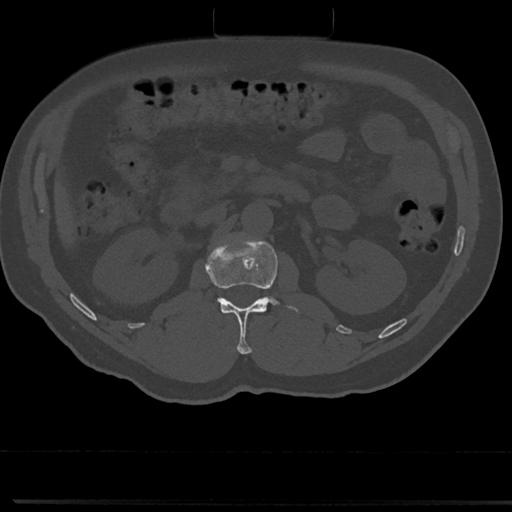
CT including the spine, one axial slice; position 69 of 817 along the scan axis; reconstruction kernel Br40s/3; bone window (W 1800 / L 400 HU); 0.5 mm slice thickness; 512 × 512 image matrix. Patient: male, 61 years. Case-level facts recorded for this patient, not image findings: primary cancer: prostate.
Structures marked on this image (semi-automatically segmented with operator editing):
- L1 vertebra: box from (x=207, y=235) to (x=302, y=354) px